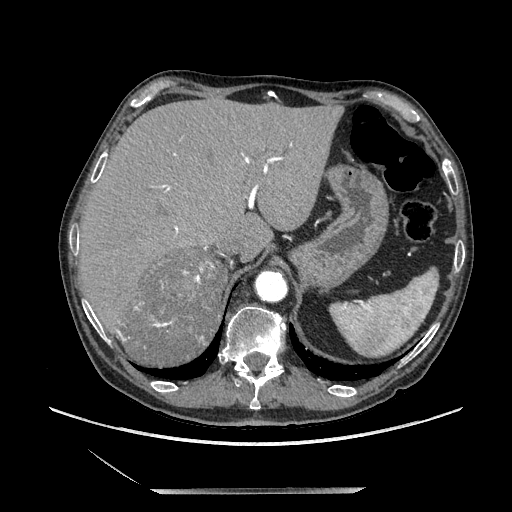
Contrast-enhanced abdominal CT, one axial slice; position 163 of 243 along the scan axis; soft-tissue window (W 400 / L 40 HU); 512 × 512 image matrix, field of view 420 × 420 mm. Male patient. From the clinical record (not read from this slice): diagnosis: adrenocortical carcinoma; tumour side: right adrenal; tumour size at pathology: 16 cm; Ki-67 index: 17 %; stage (as recorded): 3.
Structures marked on this image (semi-automatic segmentation, software-assisted and operator-edited):
- mass: box from (x=120, y=252) to (x=225, y=365) px